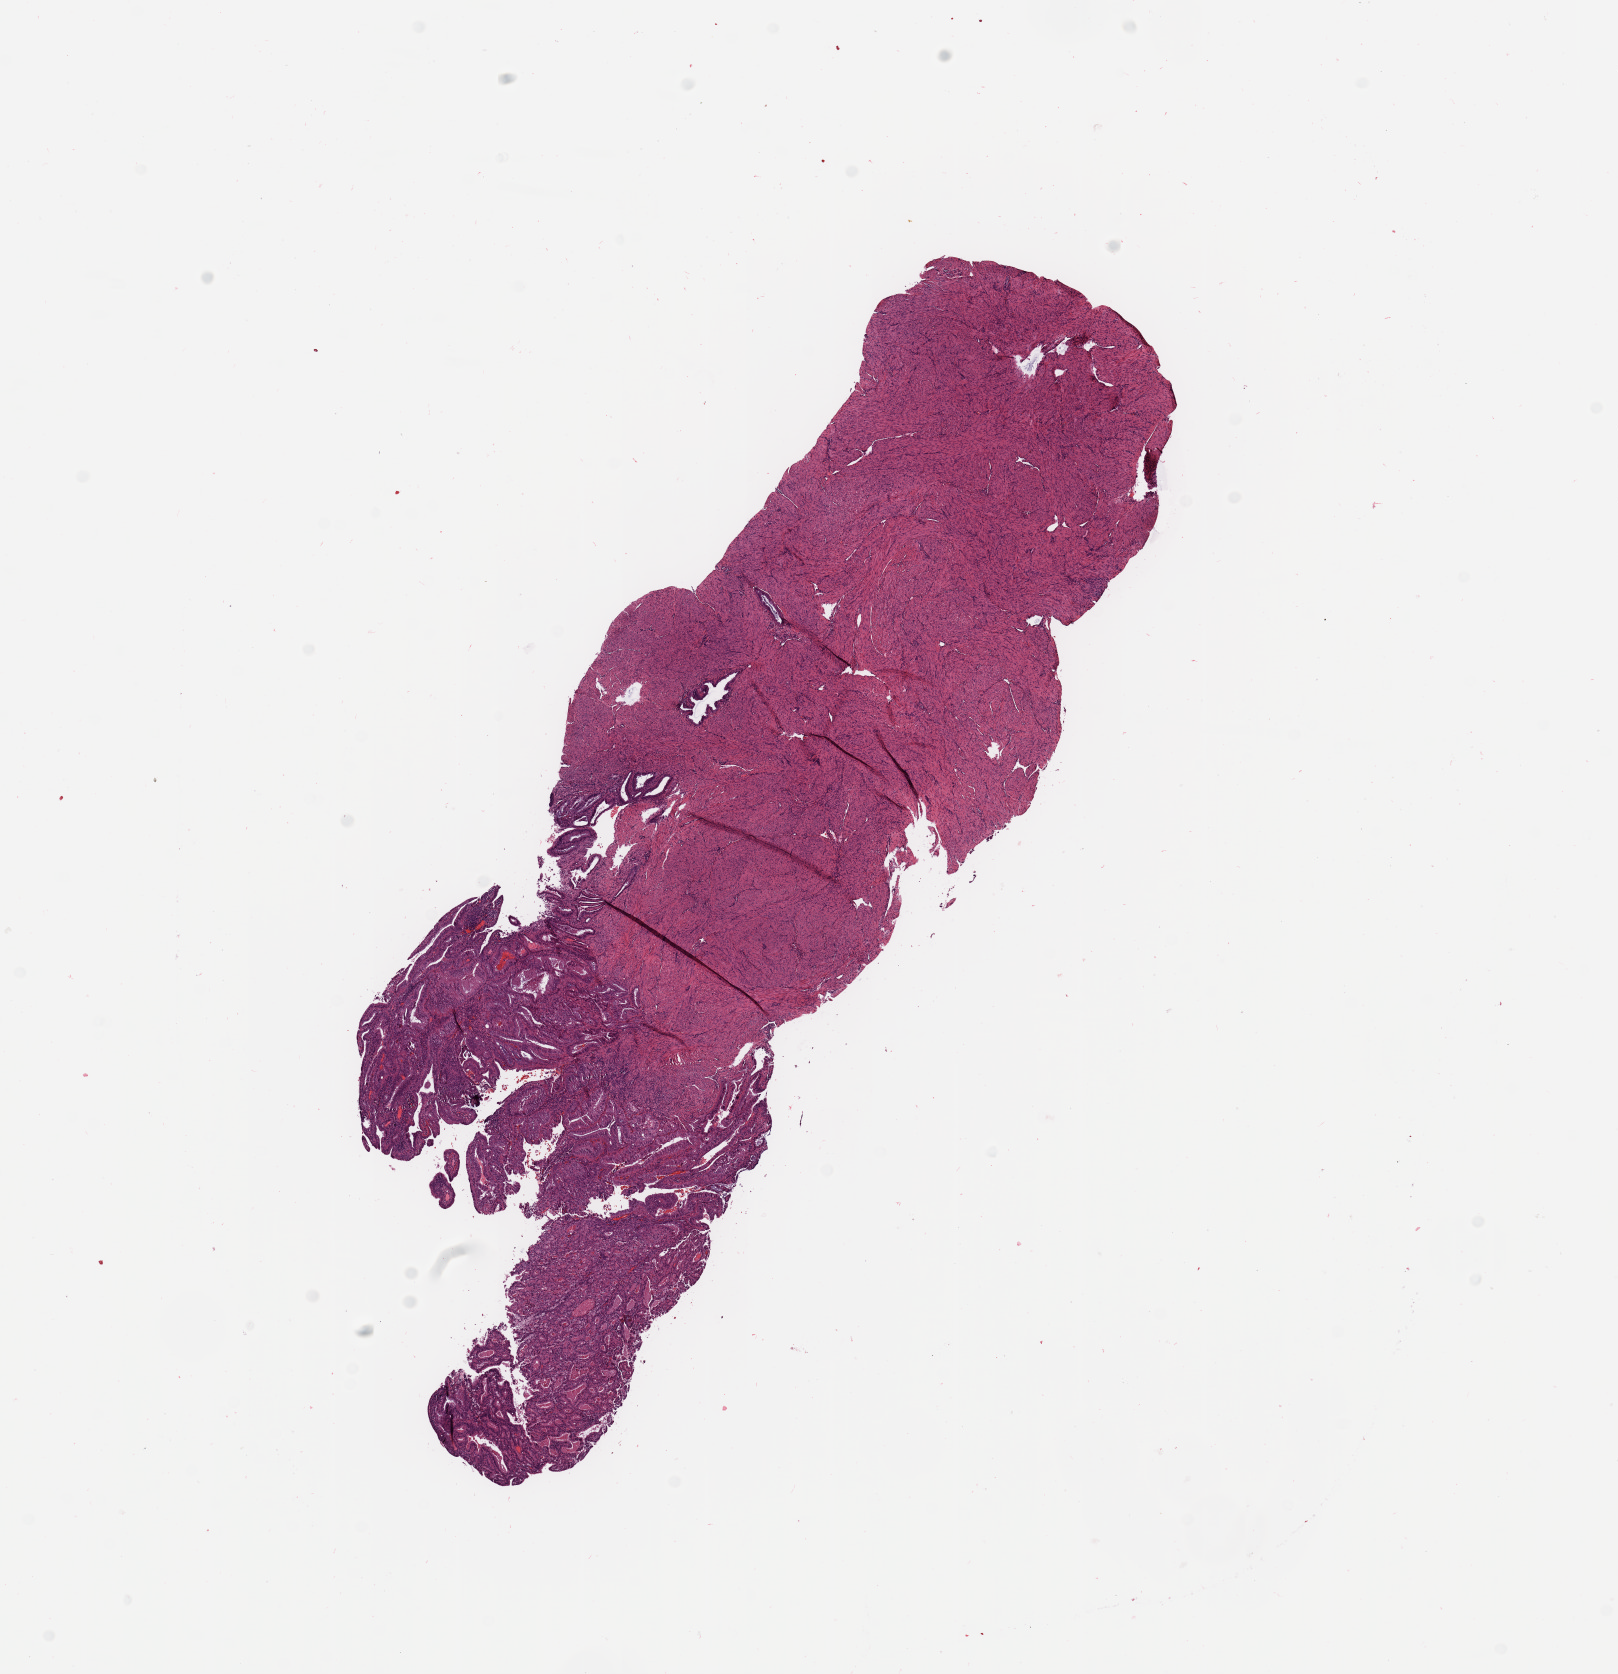
Hematoxylin and eosin (H&E) stained whole-slide image, whole scanned area (about 12.8 x 13.2 mm) shown as a low-resolution overview, tumour tissue sample, uterus. Patient: female, age 63 years. Histologic grade: G1 (well differentiated).
Histologic diagnosis: Endometrioid adenocarcinoma, NOS. AJCC pathologic stage: I.